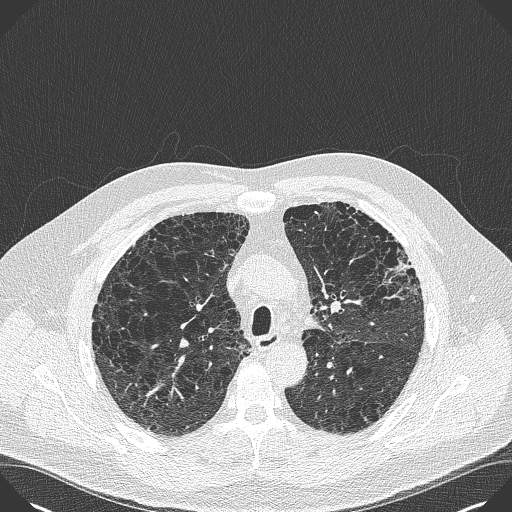
Chest CT (low-dose screening protocol), one axial image, first (baseline) screen, lung window (W 1500 / L -600 HU), 1 mm slice thickness, 120 kVp, slice 123 of 383 in the series. Male participant, aged 59 years at enrolment. Current smoker at enrolment.
Lesion marked by an expert reader, bounding box [x1, y1, x2, y2] px = [375, 238, 426, 289]. Screening reader's record for this exam: no non-calcified nodule ≥4 mm recorded.